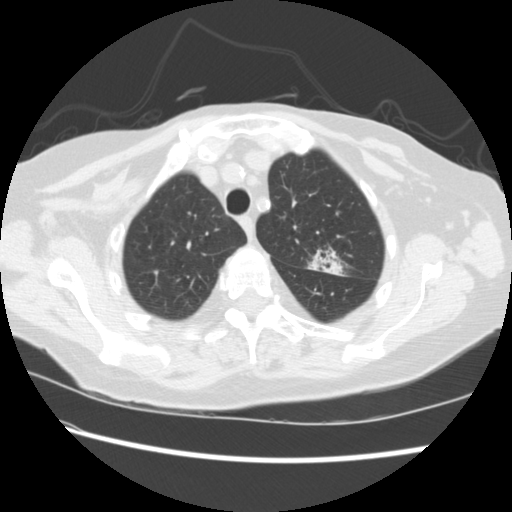
Chest CT (low-dose screening protocol), one axial image, first (baseline) screen, lung window (W 1500 / L -600 HU), 2.5 mm slice thickness, standard (soft-tissue) reconstruction kernel (STANDARD), slice 47 of 224 in the series. Female participant, aged 74 years at enrolment. Former smoker at enrolment.
Expert-annotated lung lesion, bounding box <297,242,347,282> (left, top, right, bottom; pixels). The screening reader recorded 2 non-calcified nodules or masses ≥4 mm on this exam; which of them this box marks is not recorded. Official screen result: positive, change unspecified: nodule(s) >= 4 mm or enlarging nodule(s), mass(es), or other non-specific abnormalities suspicious for lung cancer. Later outcome: lung cancer diagnosed 309 days after this screen — non-small cell carcinoma, left upper lobe, stage IV (AJCC 6th edition).